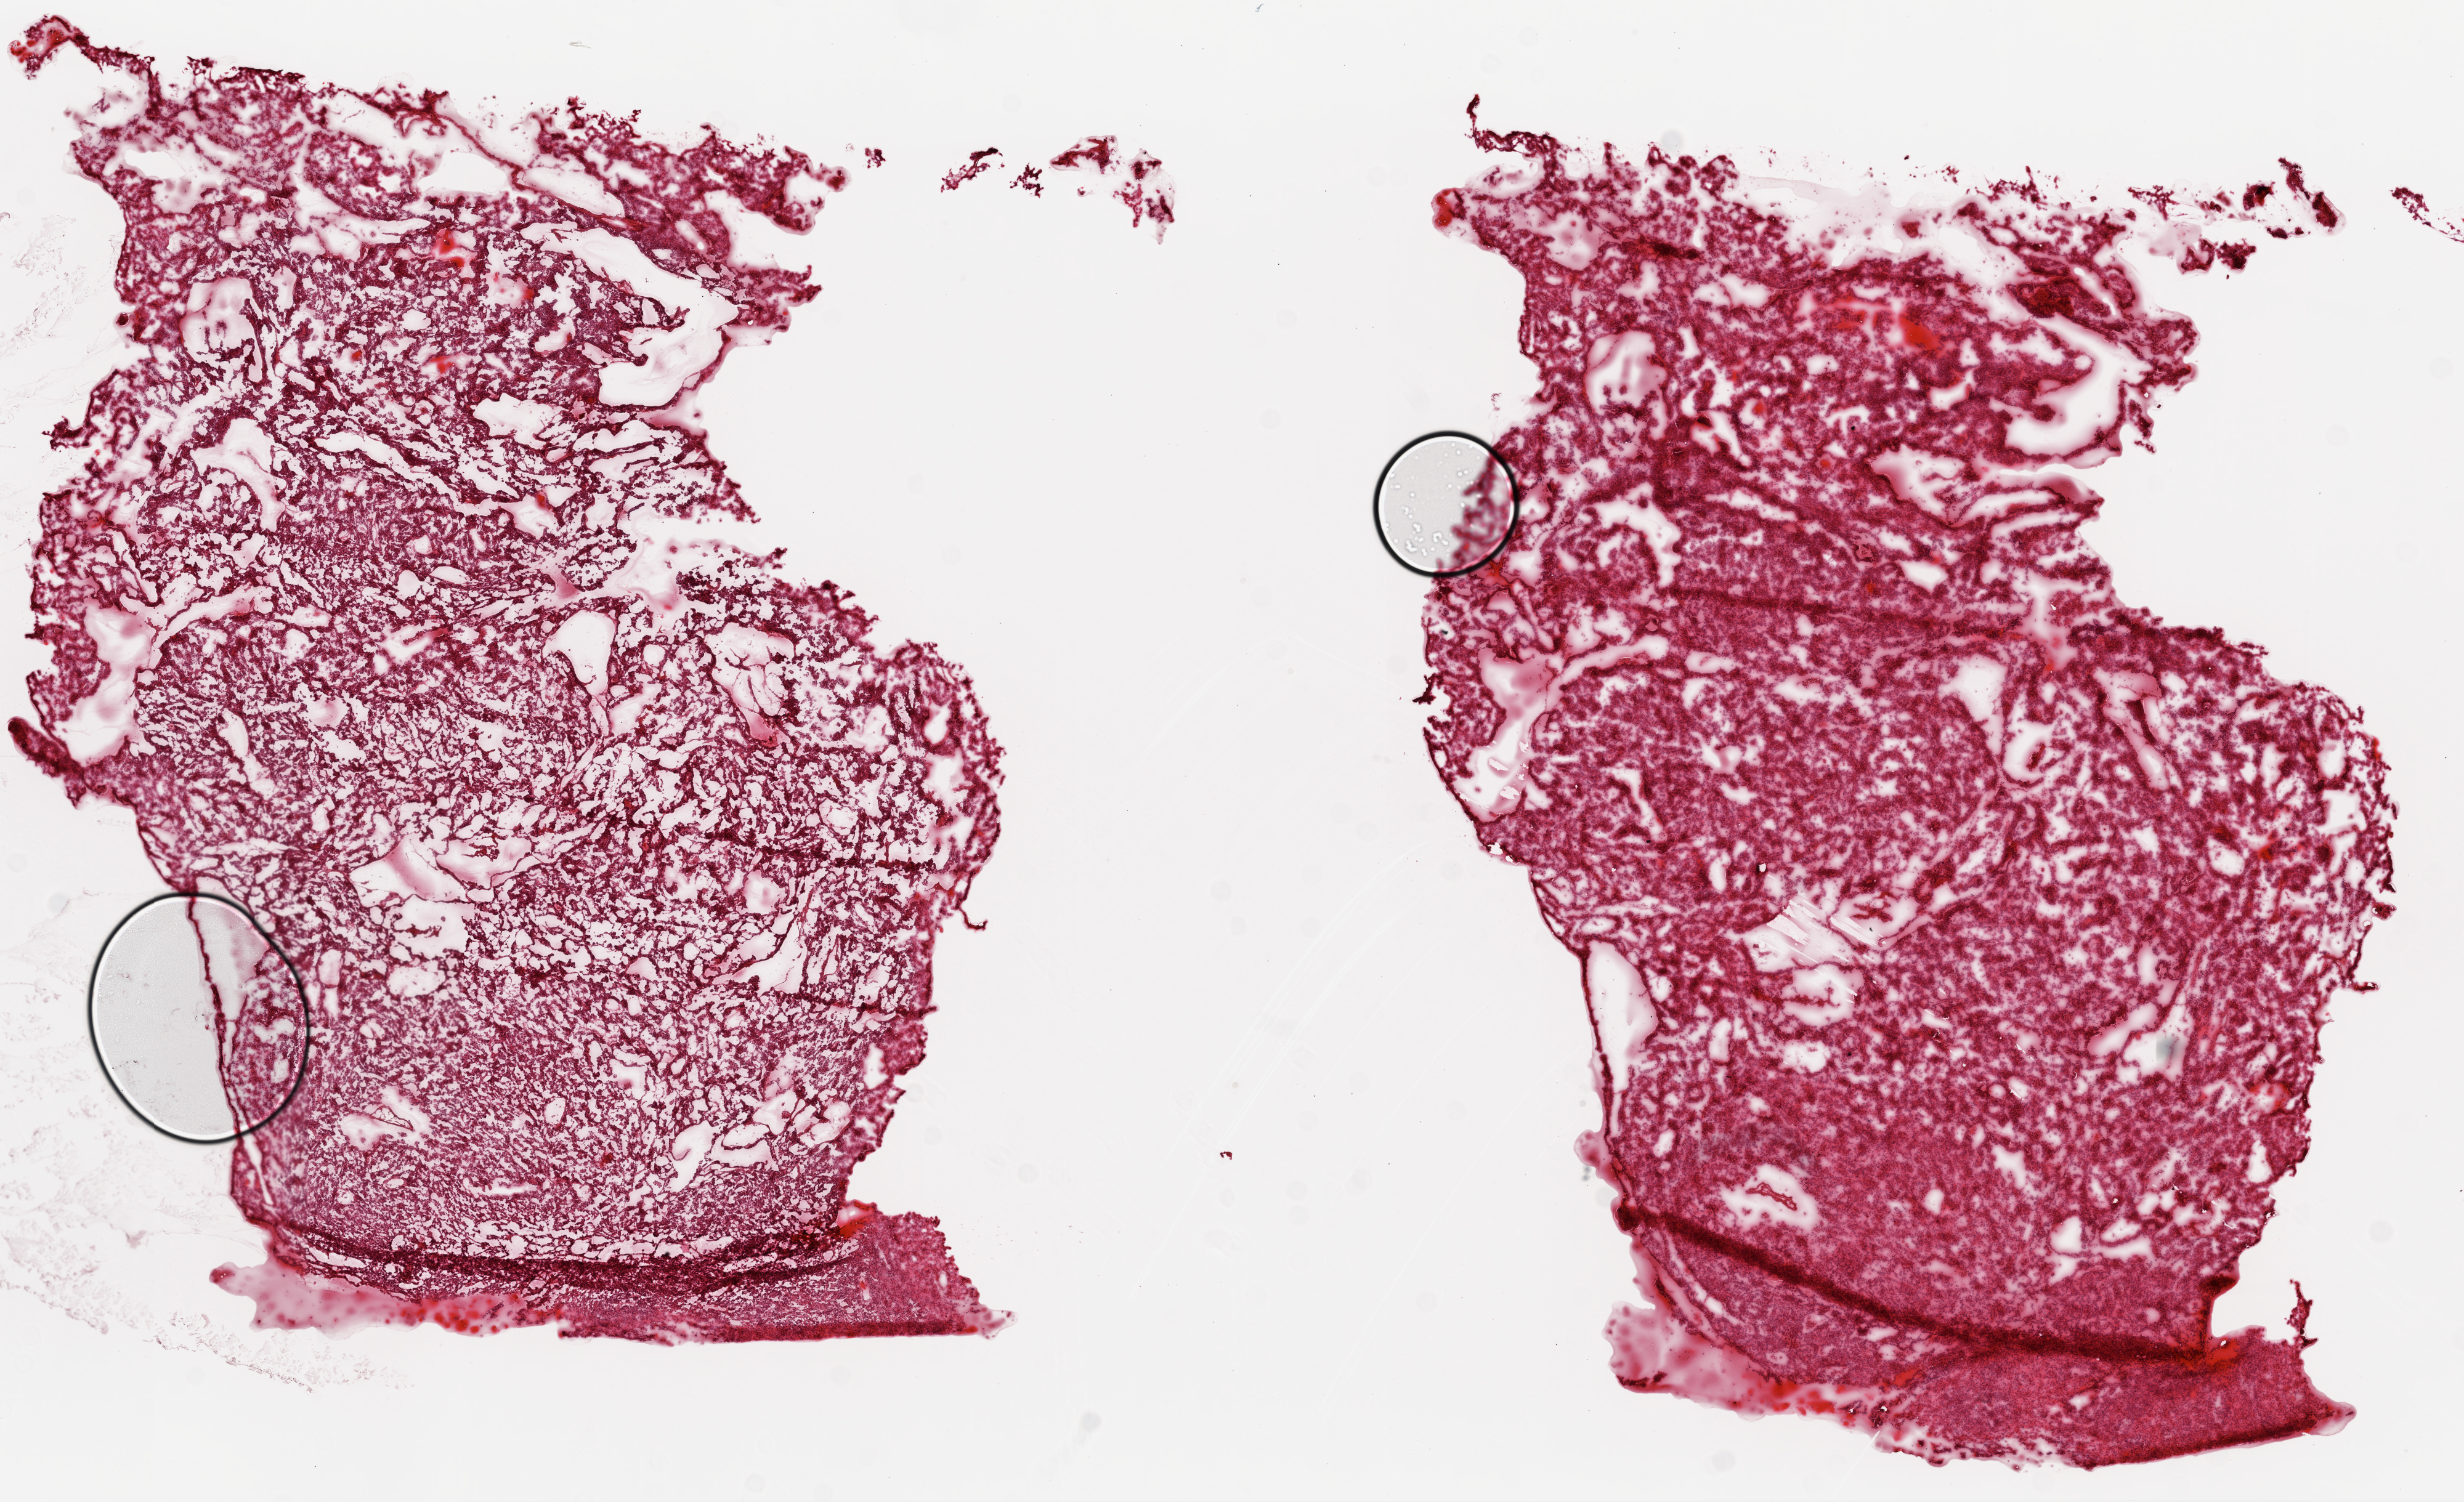
Hematoxylin and eosin (H&E) stained whole-slide image — whole scanned area (about 16.0 x 9.8 mm, slide scanned at 20x) shown as a low-resolution overview, frozen section from the top of the tissue portion, primary tumour sample from the ovary. Female patient; age at initial diagnosis 57 years.
Histologic diagnosis: Serous cystadenocarcinoma, NOS.